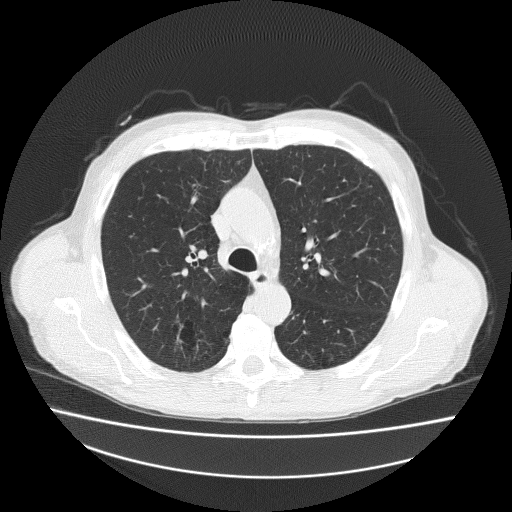
Axial slice from a low-dose chest CT screening exam; second annual screen; lung window (W 1500 / L -600 HU); 2 mm slice thickness; slice 67 of 186 in the series; 512 × 512 image matrix, field of view 408 × 408 mm. Male participant, aged 73 years at enrolment. Current smoker at enrolment.
• Lesion marked by an expert reader, box from (x=162, y=316) to (x=218, y=364) px.
• Screening reader's record for this exam: no non-calcified nodule ≥4 mm recorded.
• Lung cancer was diagnosed 418 days after this screen (after the third annual screen): adenosquamous carcinoma, right upper lobe, well differentiated (G1), stage IA (AJCC 6th edition), 20 mm at pathology.